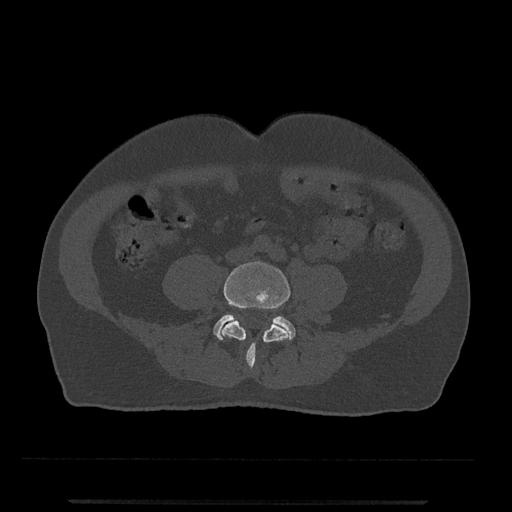
CT including the spine, one axial slice; slice 112 of 797 in the series (ordered by position); reconstruction kernel Br40s/3; 120 kVp; bone window (W 1800 / L 400 HU); 0.5 mm slice thickness; 512 × 512 image matrix, field of view 419 × 419 mm. Male patient, age 63 years. Case-level facts recorded for this patient, not image findings: primary cancer: prostate.
Outlined on this slice (semi-automatic segmentation, software-assisted and operator-edited):
- L4 vertebra: bounding box [x1, y1, x2, y2] px = [222, 261, 290, 370]
- L5 vertebra: [213, 314, 295, 340]